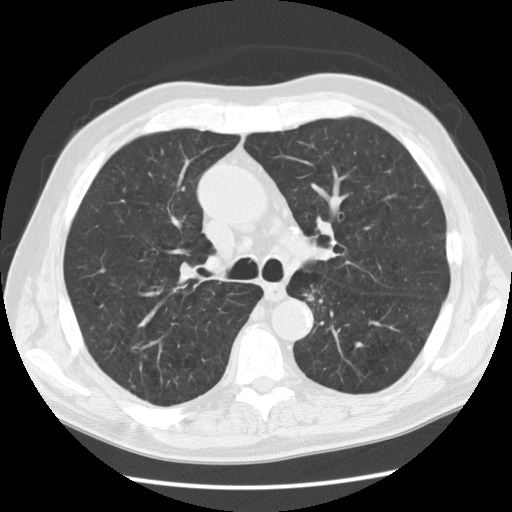
Axial slice from a low-dose chest CT screening exam. Second annual screen. Lung window (W 1500 / L -600 HU). Slice 47 of 130 in the series. Male participant, aged 73 years at enrolment. Current smoker at enrolment.
Expert reader's lesion annotation, bounding box (x1, y1, x2, y2) in pixels: (291, 273, 340, 319). The screening reader recorded 4 non-calcified nodules or masses ≥4 mm on this exam (right upper lobe, right upper lobe, left upper lobe, right lower lobe); which of them this box marks is not recorded. Lung cancer was diagnosed 302 days after this screen: small cell carcinoma, NOS, left lower lobe, stage IIIB (AJCC 6th edition), 55 mm at pathology.